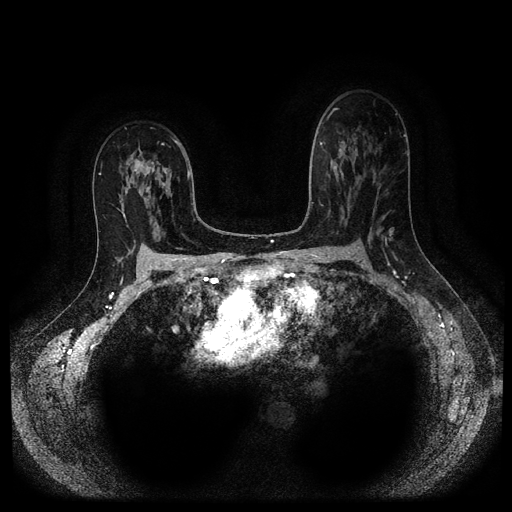
Breast MRI (dynamic contrast-enhanced, multi-phase), one axial slice; position 62 of 116 along the scan axis; dynamic contrast-enhanced series, time point 2 of 5 at this slice position (early post-contrast); 1.5 T; TE 2.6 ms, TR 5.3 ms; 2.2 mm slice thickness; 512 × 512 image matrix, field of view 340 × 340 mm. Female patient, age 50 years.
Annotated regions visible in this slice (semi-automatically segmented with operator editing):
- breast lesion (labelled 'tumour' in the annotation; benign lesions carry a separate 'benign' label): bounding box (x1, y1, x2, y2) in pixels: (131, 145, 161, 181)